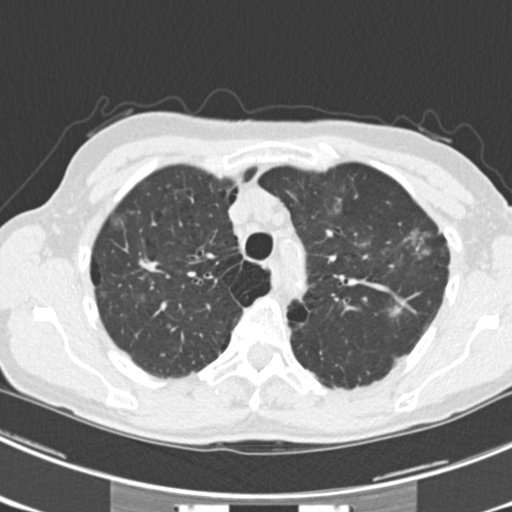
Axial slice from a low-dose chest CT screening exam. Third annual screen. Lung window (W 1500 / L -600 HU). Slice 54 of 225 in the series. Female, age 63 years at enrolment. Current smoker at enrolment.
Expert reader's lesion annotation, box from (x=379, y=216) to (x=454, y=277) px. The screening reader recorded 9 non-calcified nodules or masses ≥4 mm on this exam (left upper lobe, right upper lobe, left upper lobe, left lower lobe, right middle lobe, left lower lobe, left lower lobe, right lower lobe, right lower lobe); which of them this box marks is not recorded. Official screen result: positive, other. Lung cancer was diagnosed 15 days after this screen: bronchiolo-alveolar adenocarcinoma, NOS, right upper lobe, right middle lobe, right lower lobe, left upper lobe, left lower lobe, moderately differentiated (G2), stage IV (AJCC 6th edition).